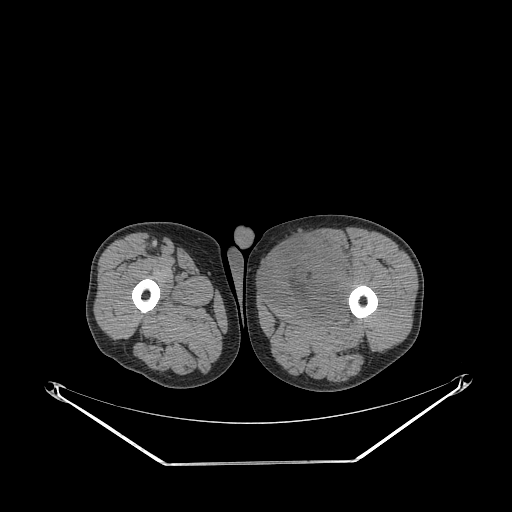
CT of an extremity soft-tissue mass (from a PET/CT study), one axial slice. Position 249 of 267 along the scan axis. Reconstruction kernel STANDARD. 140 kVp. Soft-tissue window (W 400 / L 40 HU). 3.75 mm slice thickness. 512 × 512 image matrix, field of view 500 × 500 mm. Male patient. Case-level facts recorded for this patient, not image findings: histological type: pleiomorphic liposarcoma; grade: high; site of the primary tumour: left thigh.
Structures marked on this image (expert contour drawn on MRI and transferred to this co-registered scan by the dataset authors):
- gross tumour volume including surrounding oedema: bounding box [x1, y1, x2, y2] px = [265, 235, 355, 316]
- gross tumour volume (mass): [265, 235, 353, 316]